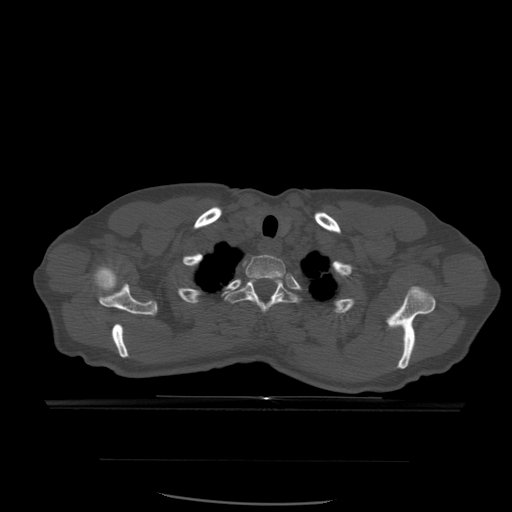
CT including the spine, one axial slice. Slice 461 of 574 in the series (ordered by position). Bone window (W 1800 / L 400 HU). 512 × 512 image matrix, field of view 392 × 392 mm. Patient age 48 years. Case-level facts recorded for this patient, not image findings: primary cancer: lung; vertebrae with lytic lesions (as recorded): T11.
Structures marked on this image (semi-automatic segmentation, software-assisted and operator-edited):
- T1 vertebra: bounding box (x1, y1, x2, y2) in pixels: (247, 255, 286, 298)
- T2 vertebra: (225, 278, 300, 316)